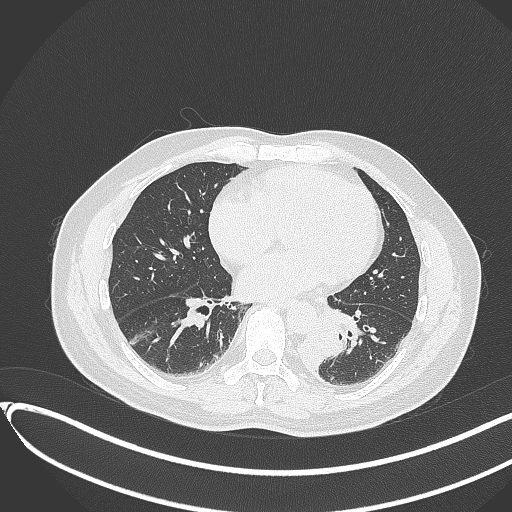
Chest CT, one axial slice. Slice 134 of 417 in the series (ordered by position). Reconstruction kernel B70f. 120 kVp. Lung window (W 1500 / L -600 HU). 1 mm slice thickness. 512 × 512 image matrix, field of view 400 × 400 mm. Male patient, age 54 years. From the clinical record (not read from this slice): clinical TNM (as recorded): T3 N0 M0.
Structures marked on this image (bounding box drawn by a radiologist):
- lung tumour (recorded histology: squamous cell carcinoma): bounding box (x1, y1, x2, y2) in pixels: (291, 323, 344, 371)